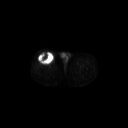
FDG PET of an extremity soft-tissue mass (from a PET/CT study), one axial slice; position 280 of 311 along the scan axis; 3.27 mm slice thickness; 128 × 128 image matrix, field of view 700 × 700 mm. Patient: male, 56 years. Case-level facts recorded for this patient, not image findings: histological type: pleiomorphic leiomyosarcoma; grade: intermediate; site of the primary tumour: right thigh.
Annotated regions visible in this slice (expert contour drawn on MRI and transferred to this co-registered scan by the dataset authors):
- gross tumour volume including surrounding oedema: box from (x=38, y=52) to (x=55, y=65) px
- gross tumour volume (mass): (x=38, y=52)–(x=55, y=65)